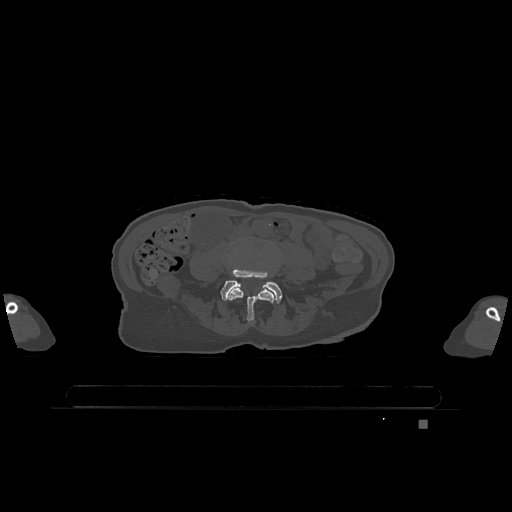
CT including the spine, one axial slice. Slice 268 of 1317 in the series (ordered by position). Bone window (W 1800 / L 400 HU). 512 × 512 image matrix, field of view 500 × 500 mm. Patient: female, 74 years. From the clinical record (not read from this slice): primary cancer: lung.
Outlined on this slice (semi-automatic segmentation, software-assisted and operator-edited):
- L4 vertebra: bounding box [x1, y1, x2, y2] px = [228, 282, 275, 322]
- L5 vertebra: [220, 269, 282, 304]